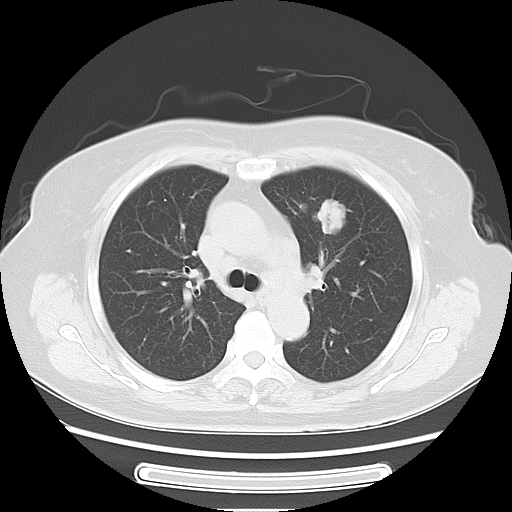
Chest CT, one axial slice; position 41 of 57 along the scan axis; 120 kVp; lung window (W 1500 / L -600 HU); 512 × 512 image matrix, field of view 363 × 363 mm. Patient: female, 77 years. From the clinical record (not read from this slice): clinical TNM (as recorded): T1c N3 M0.
Annotated regions visible in this slice (rectangle marked by the reading radiologist):
- lung tumour (recorded histology: adenocarcinoma): bounding box <315,197,359,244> (left, top, right, bottom; pixels)